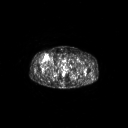
FDG PET of an extremity soft-tissue mass (from a PET/CT study), one axial slice. Slice 307 of 311 in the series (ordered by position). 3.27 mm slice thickness. 128 × 128 image matrix. Patient: male, 56 years. From the clinical record (not read from this slice): histological type: pleiomorphic leiomyosarcoma; grade: intermediate; site of the primary tumour: right thigh.
Structures marked on this image (expert contour drawn on MRI and transferred to this co-registered scan by the dataset authors):
- gross tumour volume including surrounding oedema: bounding box <43,55,49,61> (left, top, right, bottom; pixels)